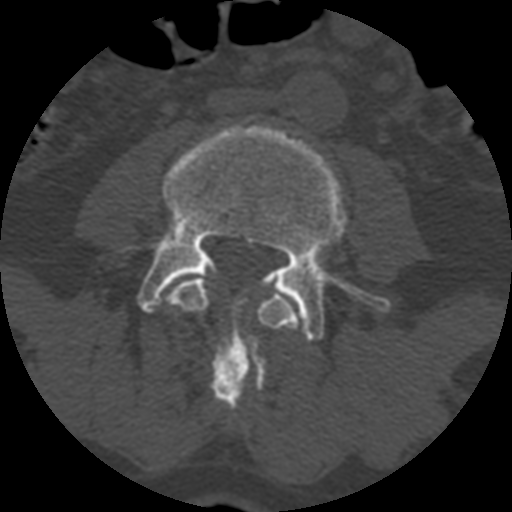
CT including the spine, one axial slice; slice 289 of 399 in the series (ordered by position); reconstruction kernel STANDARD; 120 kVp; bone window (W 1800 / L 400 HU); 512 × 512 image matrix, field of view 160 × 160 mm. Patient age 71 years. From the clinical record (not read from this slice): primary cancer: prostate.
Outlined on this slice (semi-automatic segmentation, software-assisted and operator-edited):
- L3 vertebra: box from (x=166, y=276) to (x=300, y=409) px
- L4 vertebra: (x=125, y=123)–(x=390, y=342)